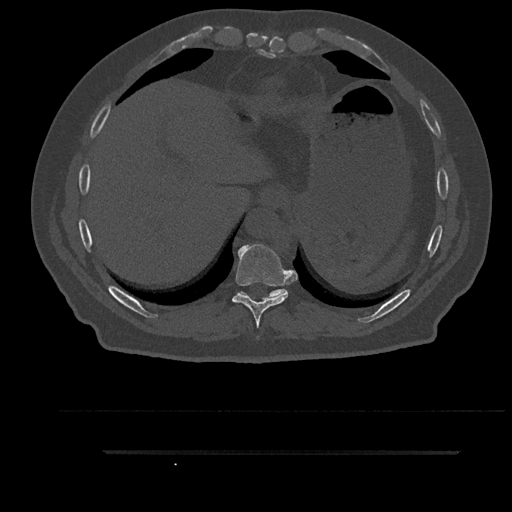
CT including the spine, one axial slice. Position 413 of 797 along the scan axis. Reconstruction kernel Br40s/3. 120 kVp. Bone window (W 1800 / L 400 HU). 0.5 mm slice thickness. 512 × 512 image matrix, field of view 432 × 432 mm. Patient: male, 63 years. From the clinical record (not read from this slice): primary cancer: renal.
Annotated regions visible in this slice (semi-automatic segmentation, software-assisted and operator-edited):
- T10 vertebra: bounding box (x1, y1, x2, y2) in pixels: (239, 289, 286, 298)
- T9 vertebra: (232, 244, 290, 328)